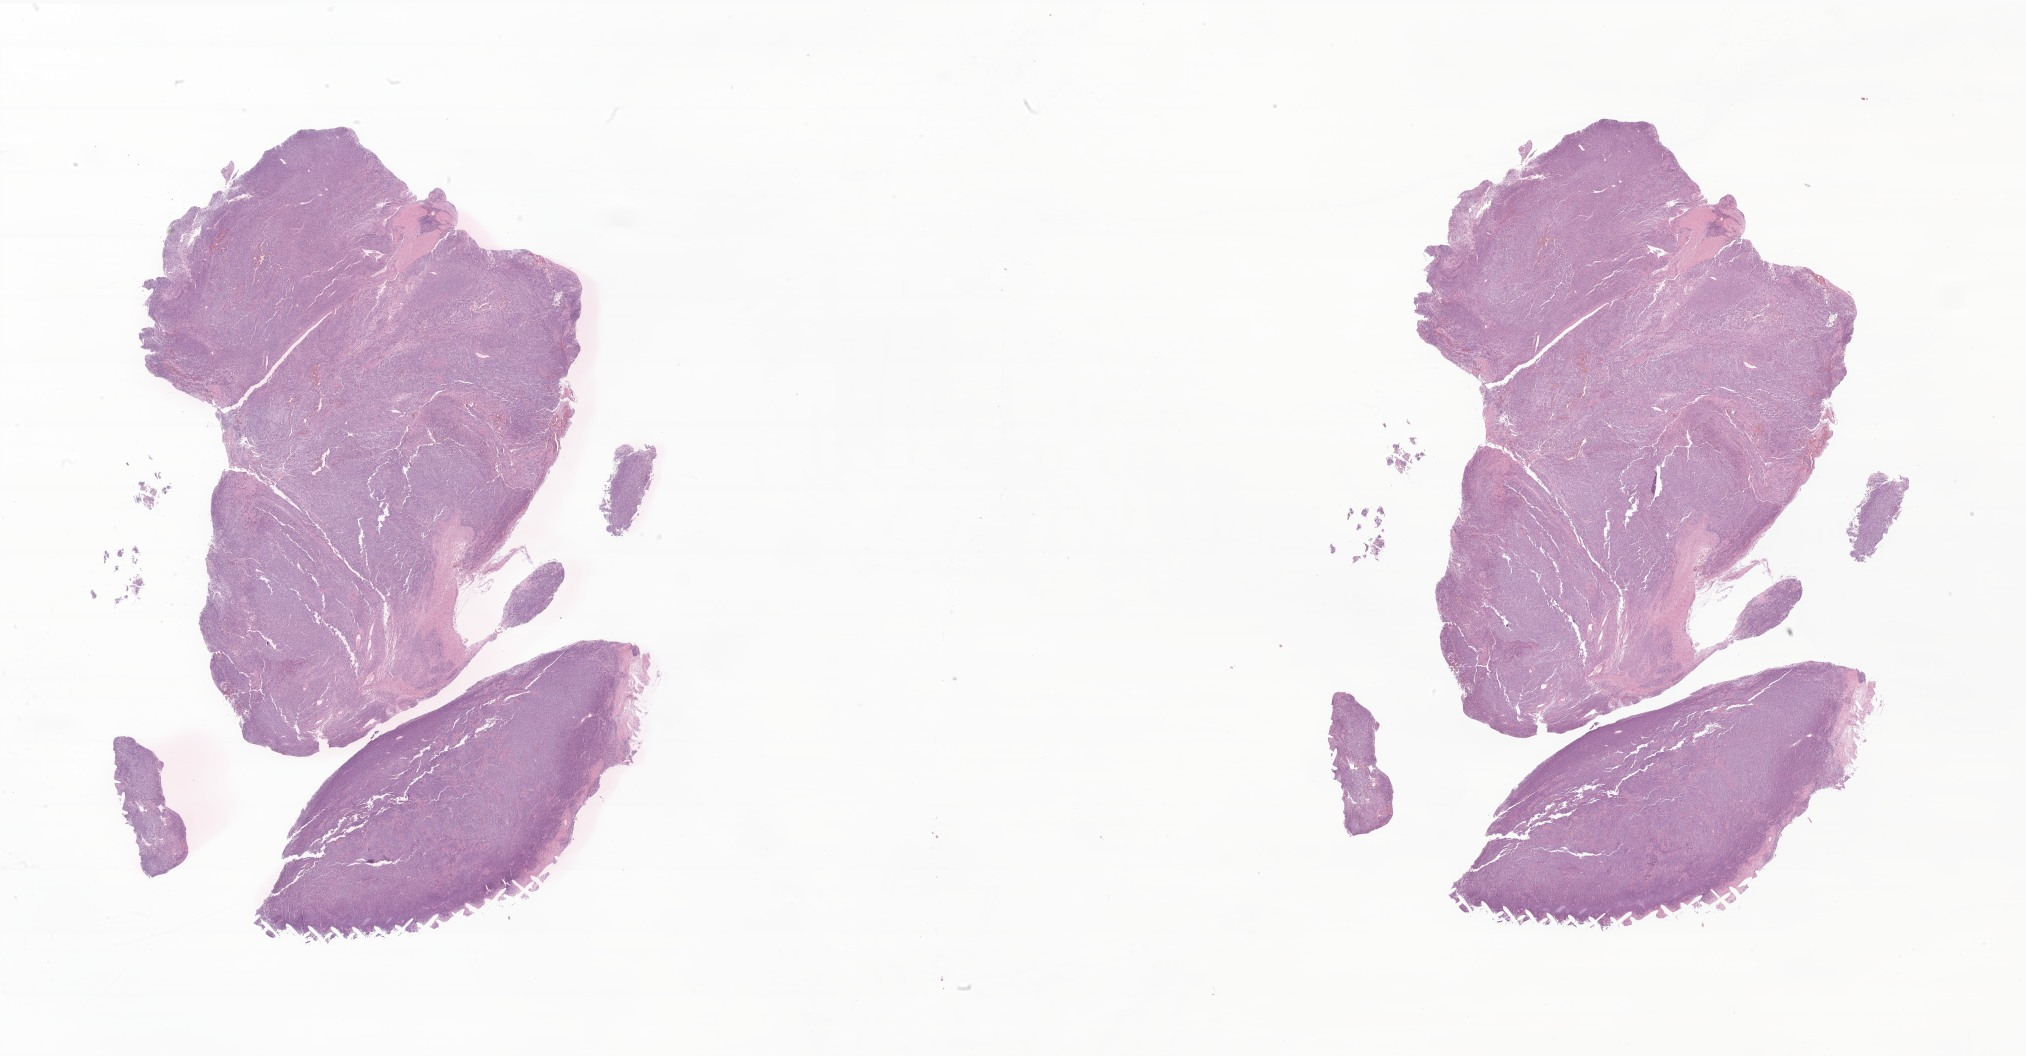
Whole-slide image, H&E stain of tumor tissue from the upper limb lymph node, shown as a low-resolution overview of the whole scanned area (about 34.2 x 17.8 mm); FFPE section. Patient male; age 207 months (17 years 3 months).
Tissue or organ of origin (case record): lymph nodes of axilla or arm. Diagnosis: Synovial sarcoma, NOS.